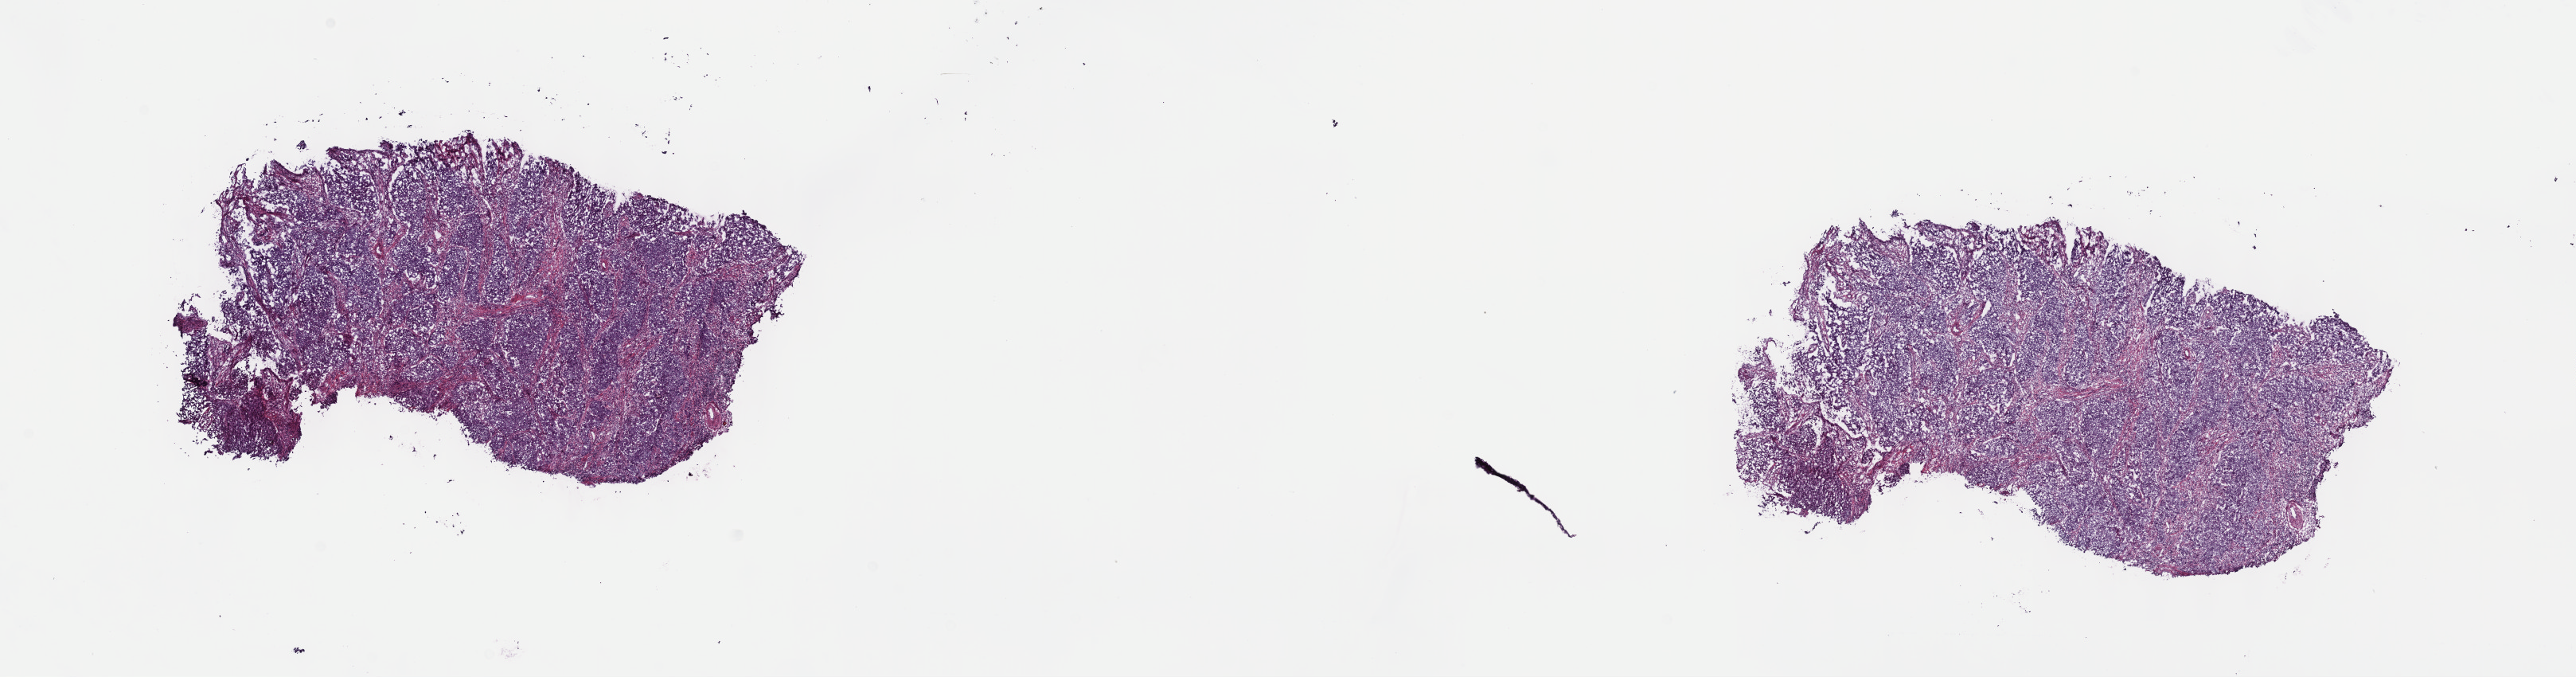
H&E-stained whole-slide image, low-resolution overview of the scanned area, about 26.2 x 6.9 mm. Frozen section from the top of the tissue portion. Primary tumour sample from the bladder. Patient: male, age at initial diagnosis 65 years. Histologic grade: high grade. Slide review estimates, as recorded: tumour cells 100%, tumour nuclei 85%, normal cells 0%, stromal cells 0%, necrosis 0%. Infiltration values recorded for this section: lymphocyte infiltration 0%, monocyte infiltration 0%, neutrophil infiltration 0%.
- histologic diagnosis: Transitional cell carcinoma
- AJCC pathologic stage: IV
- lymph nodes positive (case pathology): 3 of 6 examined